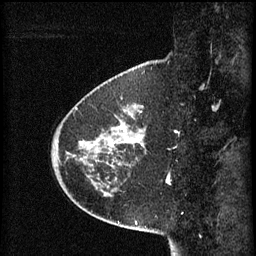
Breast MRI (dynamic contrast-enhanced), one sagittal slice; 3 images stored at this slice position (order not interpretable as contrast timing); 1.5 T; TE 4.2 ms, TR 8.2 ms; 256 × 256 image matrix. Patient: female, 45 years.
Structures marked on this image (semi-automatic segmentation, software-assisted and operator-edited):
- analysis volume of interest (the breast-tissue region the enhancement analysis was run in; not a lesion): box from (x=80, y=102) to (x=146, y=171) px
- tumour enhancement mask (voxels above the 70 % enhancement threshold inside the analysis volume of interest): (x=86, y=132)–(x=143, y=147)